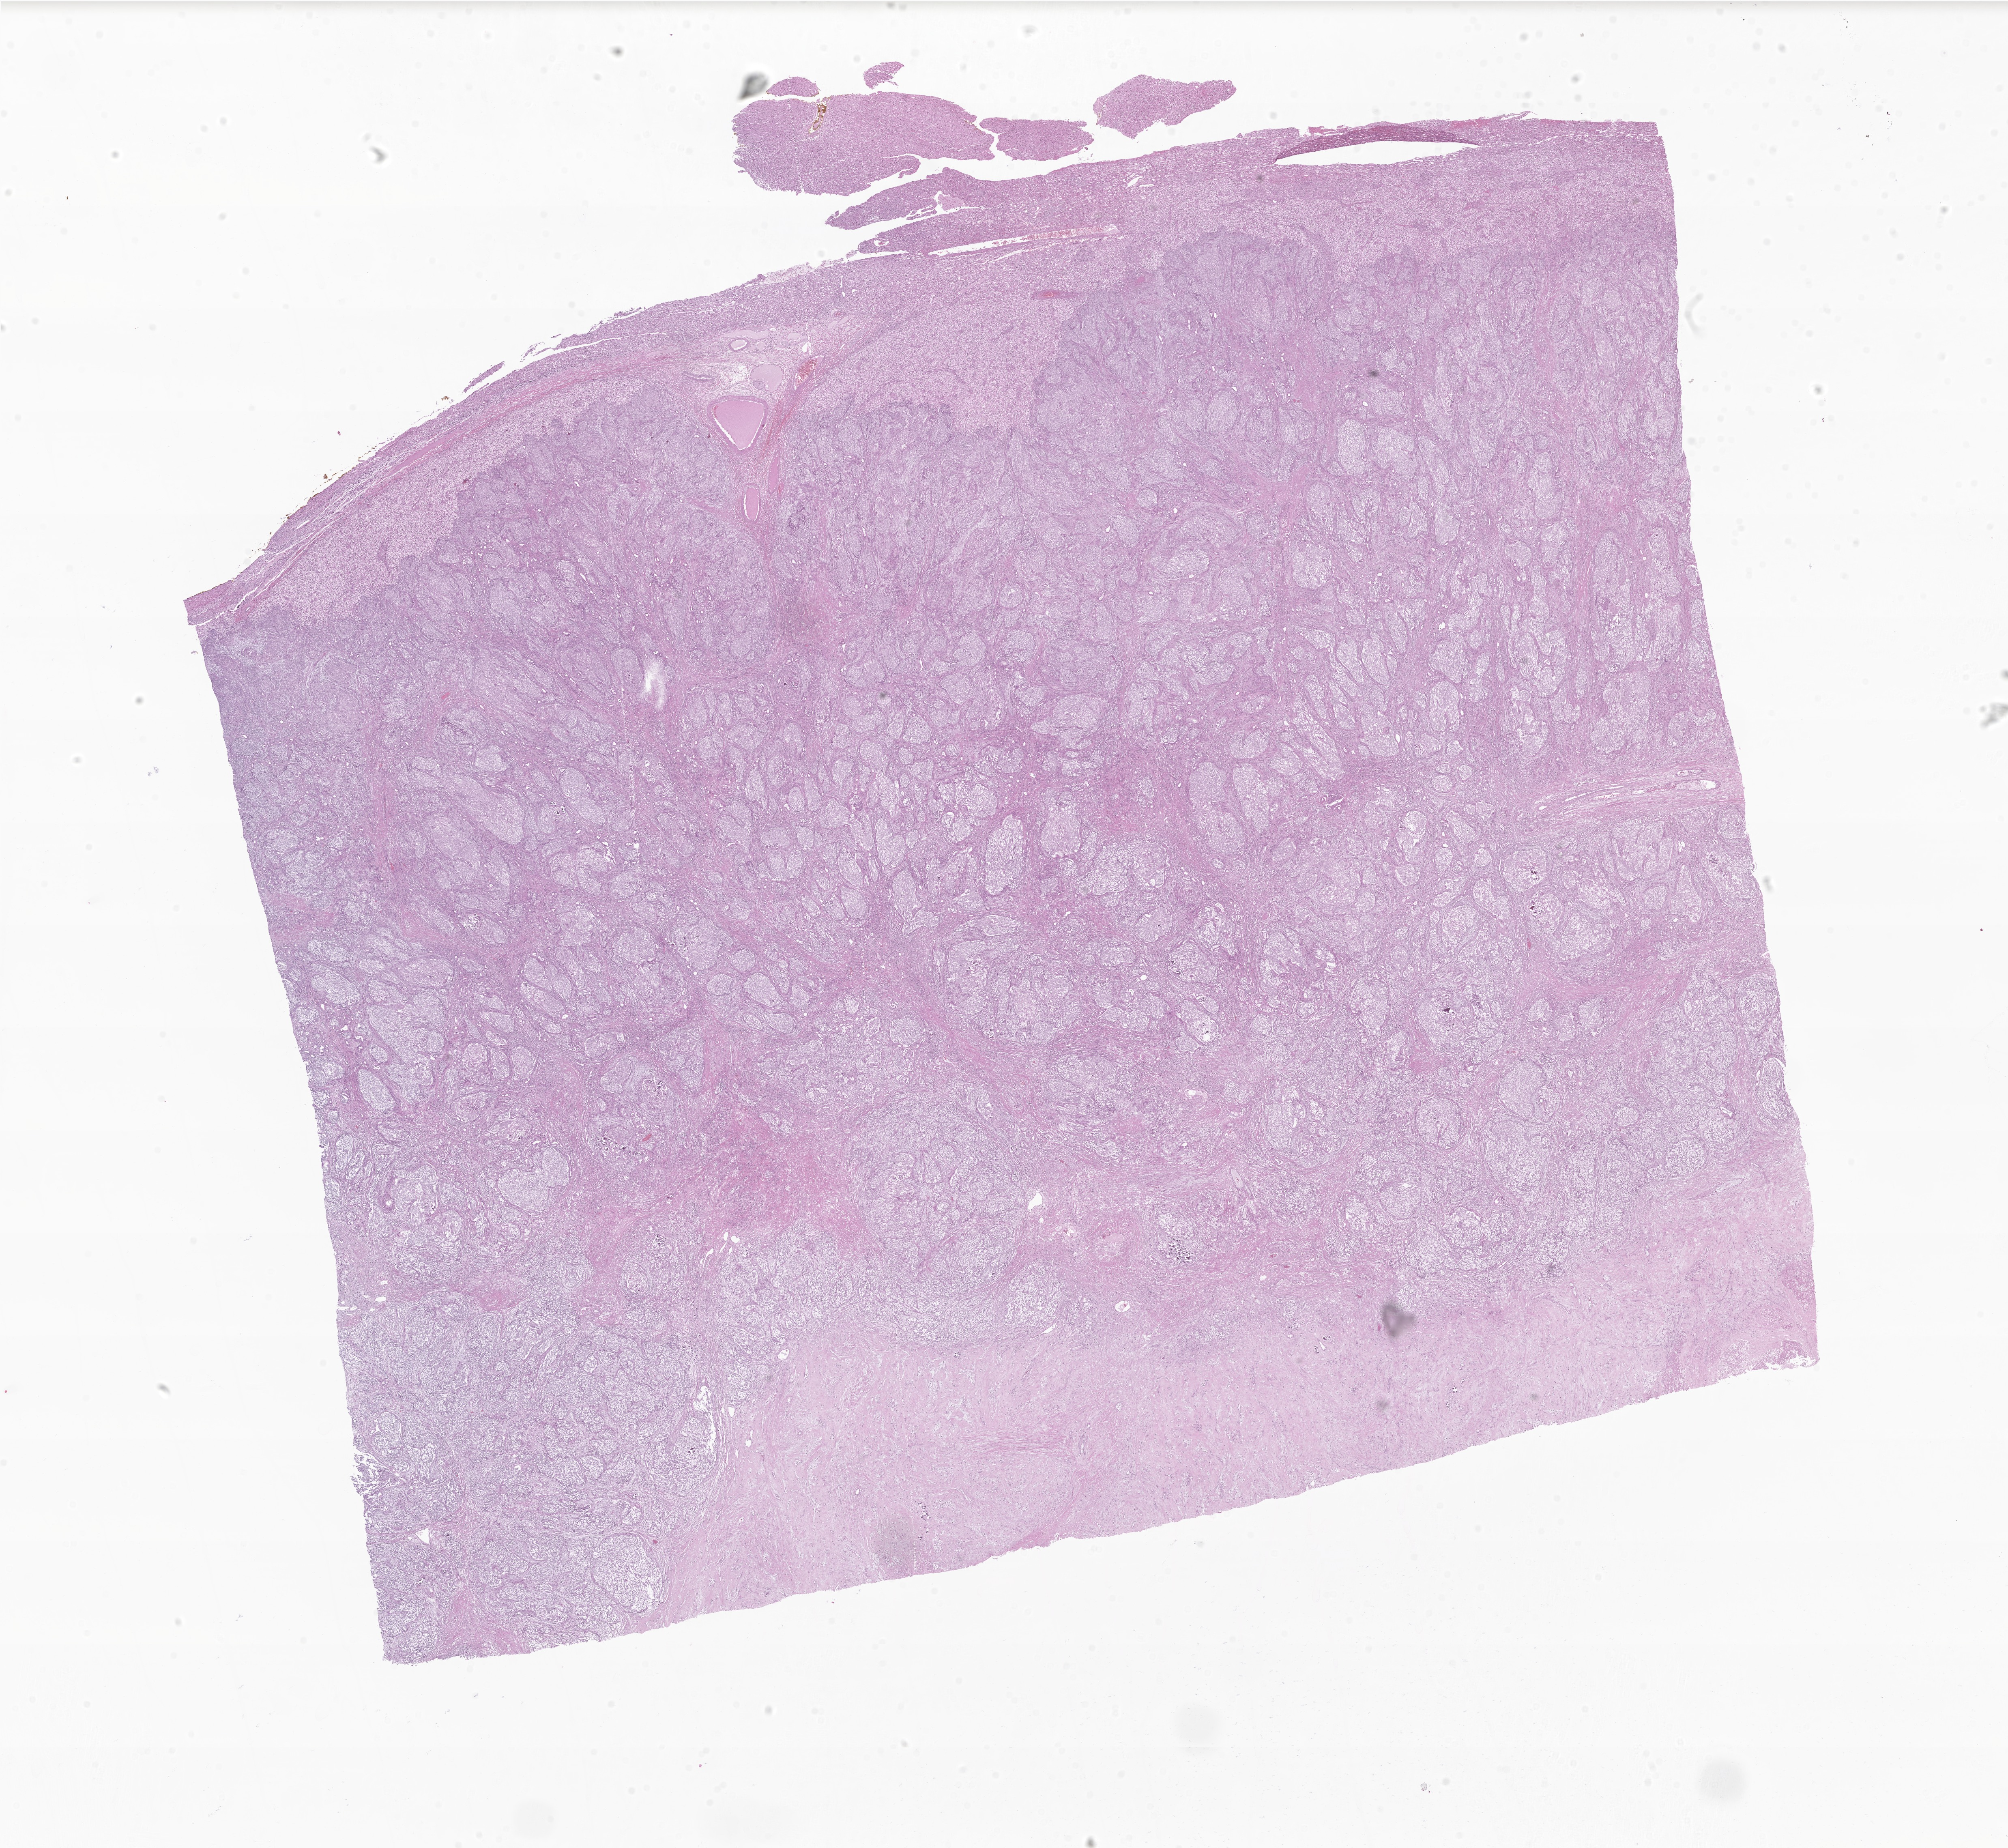
Hematoxylin and eosin (H&E) whole-slide image of tumor tissue from the liver, low-resolution overview of the scanned area, about 20.9 x 19.2 mm, formalin-fixed, paraffin-embedded (FFPE) tissue. Female patient, age 148 months (12 years 4 months).
Diagnosis (ICD-O-3 morphology term): Sex cord-gonadal stromal tumor, NOS.